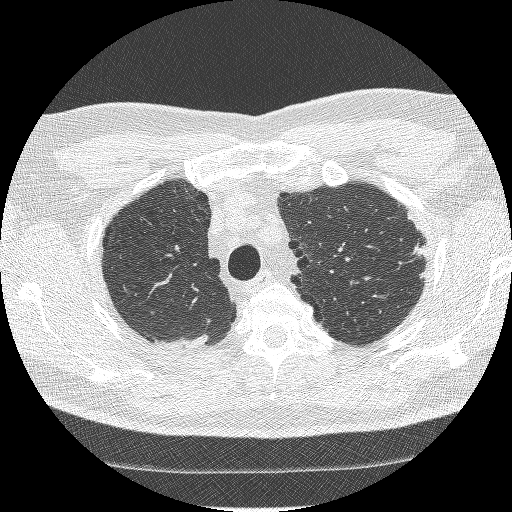
Low-dose screening chest CT, axial slice; first (baseline) screen; lung window (W 1500 / L -600 HU); 512 × 512 image matrix, field of view 335 × 335 mm. Male participant, aged 66 years at enrolment. Current smoker at enrolment.
• Expert reader's lesion annotation, bounding box [x1, y1, x2, y2] px = [399, 234, 435, 269].
• The exam's reader record, not a measurement of the box and not confirmed to be the same lesion: non-calcified nodule or mass ≥4 mm, right lower lobe, 45 × 19 mm, spiculated (stellate) margins, soft tissue attenuation.
• Note: the box lies in the patient's left hemithorax on this image, whereas the reader's record names the right lung; they may be different findings.
• Official screen result: positive, change unspecified: nodule(s) >= 4 mm or enlarging nodule(s), mass(es), or other non-specific abnormalities suspicious for lung cancer.
• Later outcome: lung cancer diagnosed 960 days after this screen (after the third annual screen) — adenocarcinoma, NOS, left upper lobe, poorly differentiated (G3), stage IB (AJCC 6th edition), 16 mm at pathology.